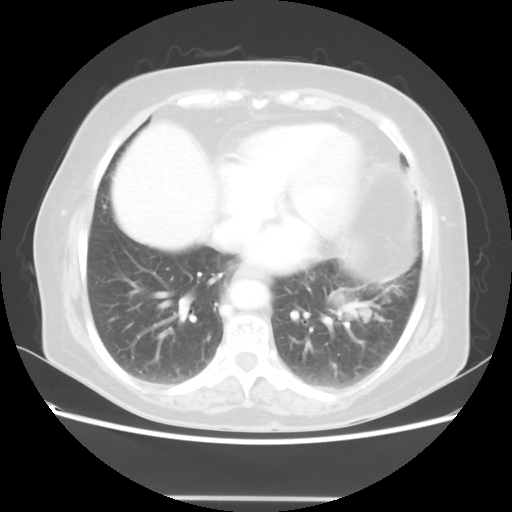
Chest CT, one axial slice; slice 21 of 56 in the series (ordered by position); lung window (W 1500 / L -600 HU); 5 mm slice thickness; 512 × 512 image matrix, field of view 360 × 360 mm. Patient: female, 73 years. Case-level facts recorded for this patient, not image findings: clinical TNM (as recorded): T1c N0 M0.
Outlined on this slice (bounding box drawn by a radiologist):
- lung tumour (recorded histology: adenocarcinoma): bounding box [x1, y1, x2, y2] px = [339, 295, 378, 323]